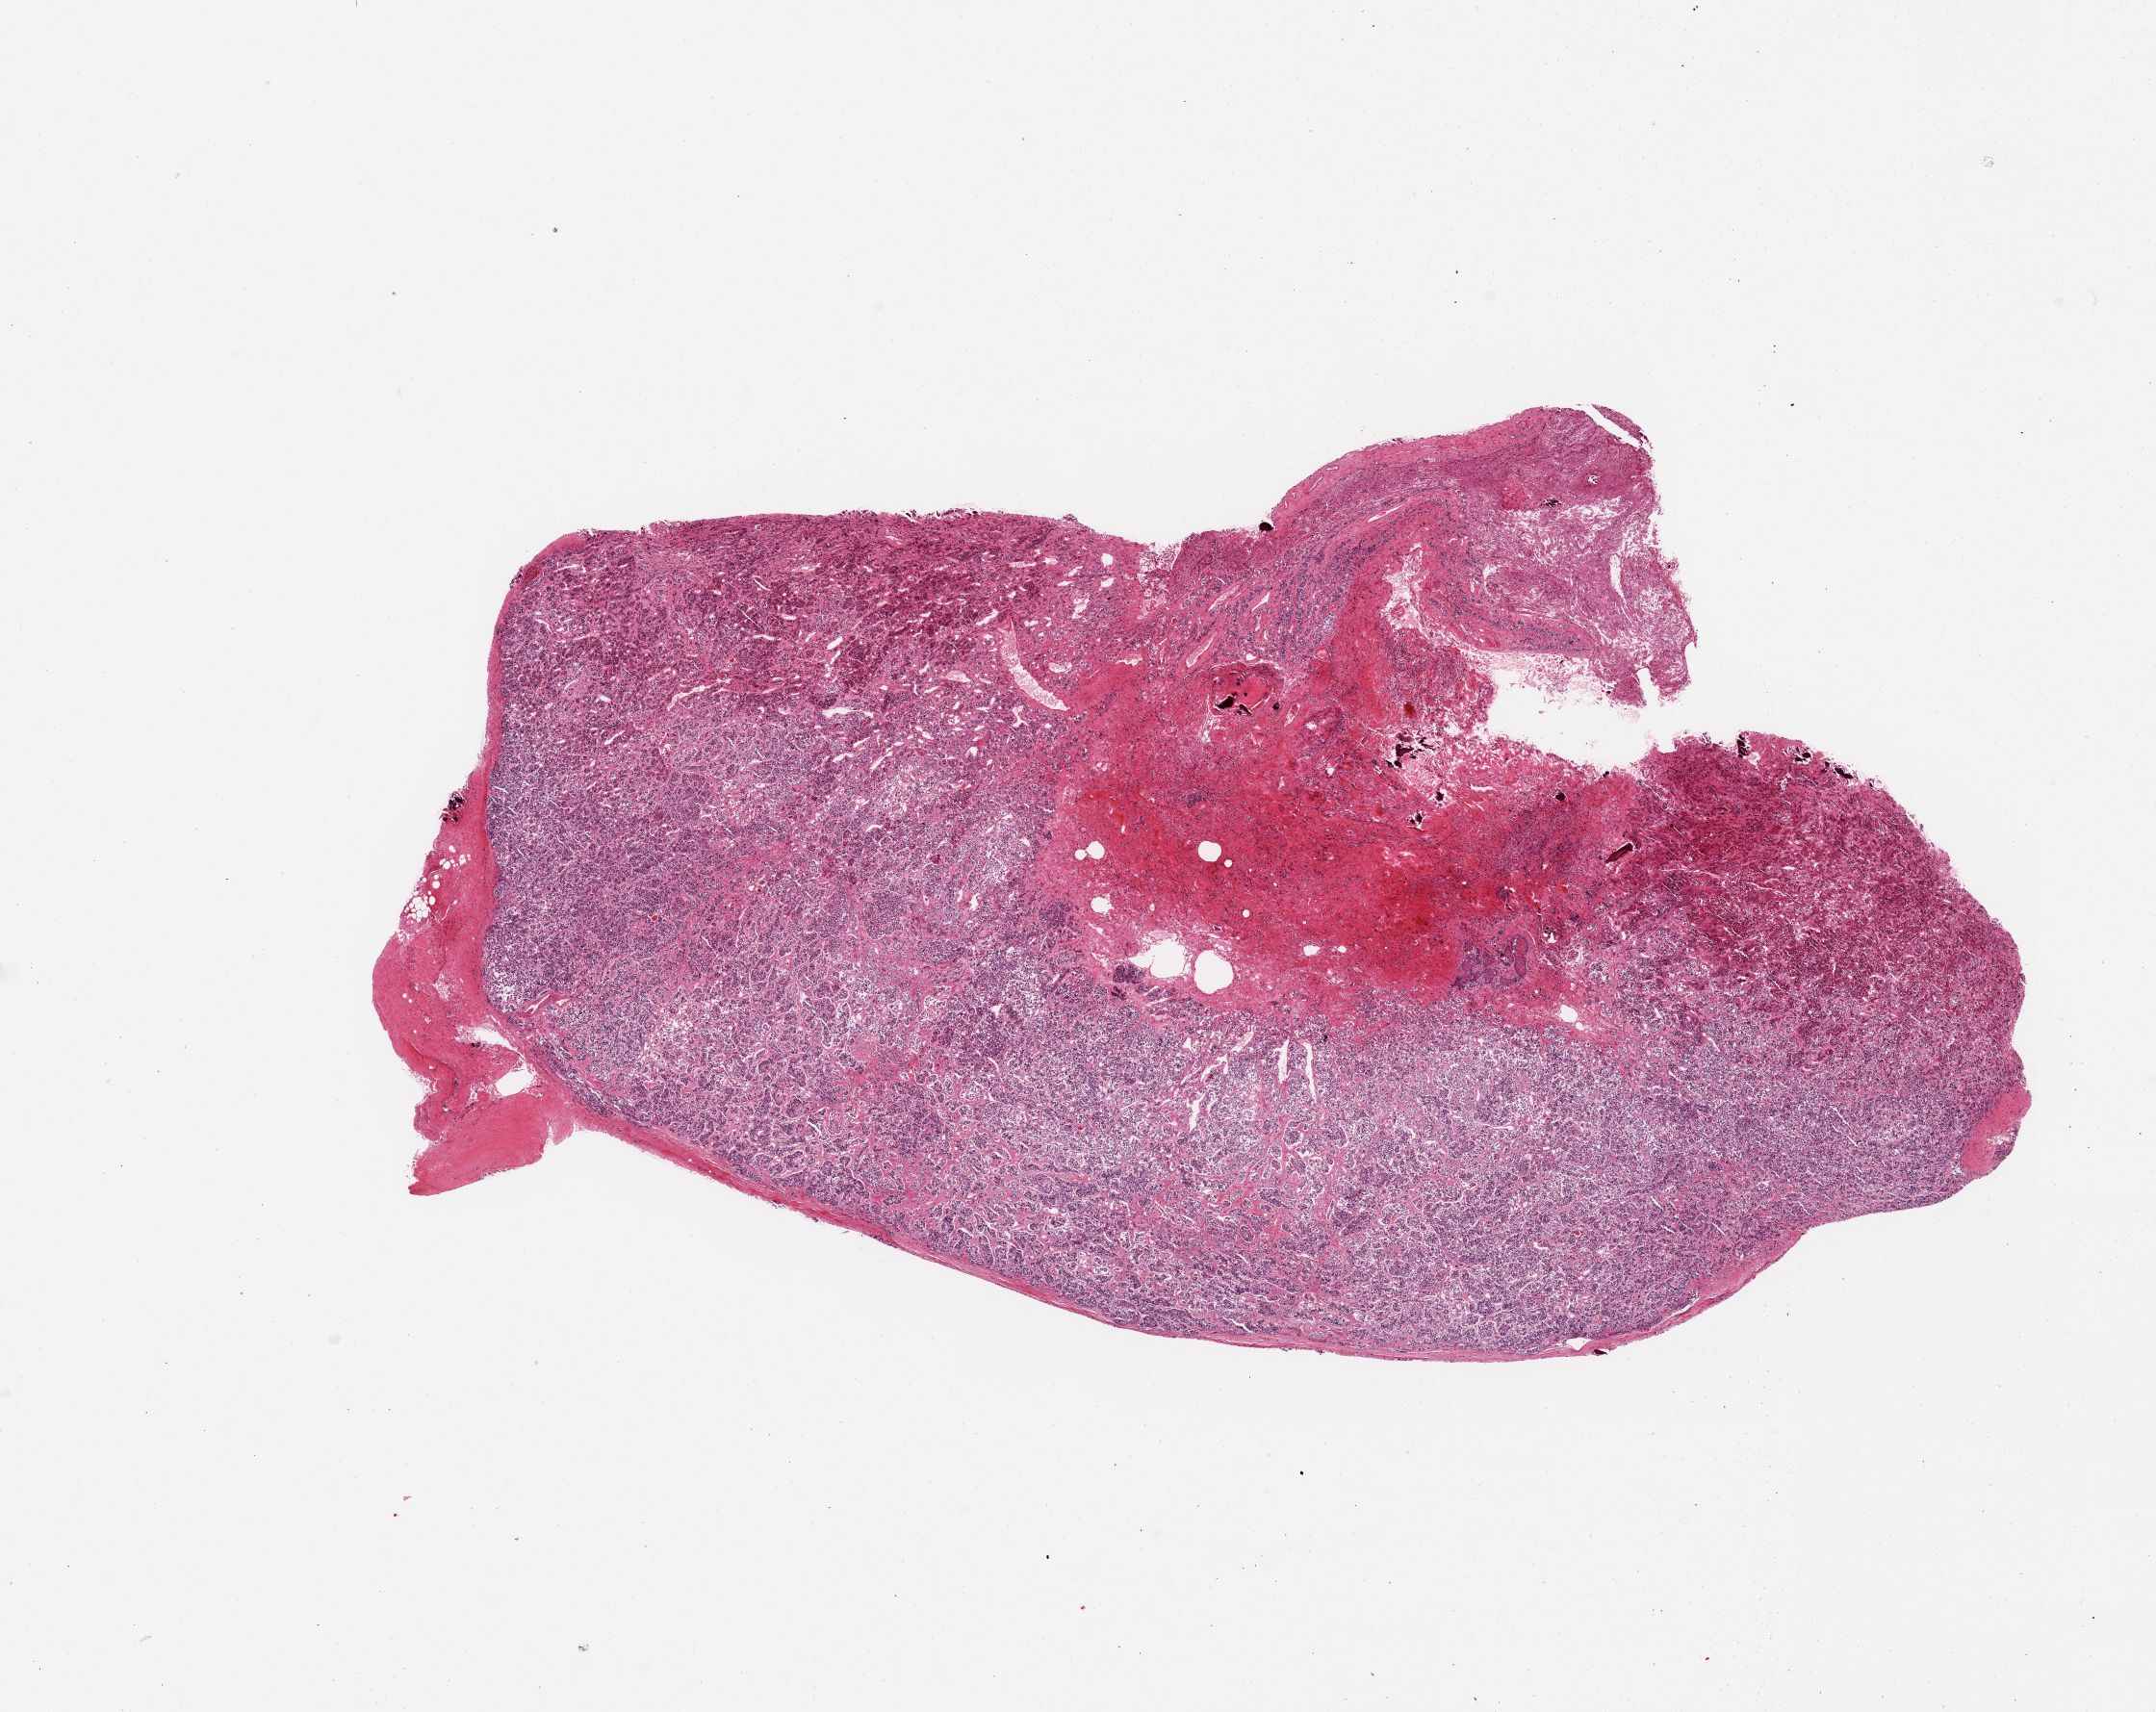
Whole-slide image, H&E stain — whole scanned area (about 17.7 x 14.1 mm, acquisition: 20x scan) shown as a low-resolution overview. PAXgene-fixed paraffin-embedded (PFPE) section. Section of pituitary (target tissue). Tissue donor sample. Male donor.
Reviewer comment on this tissue sample: 1 piece, mainly adenohypophysis; ~3mm nubbin of neurohypophysis.